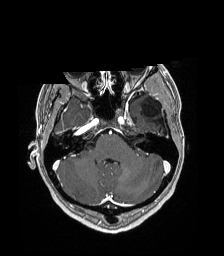
Brain MRI from a brain-tumour surgery series, one axial slice. T1-weighted post-contrast. 1 mm slice thickness. 224 × 256 image matrix, field of view 224 × 256 mm. From the clinical record (not read from this slice): histopathology: Low grade glioma; IDH mutation: no.
Outlined on this slice (expert manual segmentation):
- previous resection cavity: box from (x=143, y=101) to (x=161, y=117) px